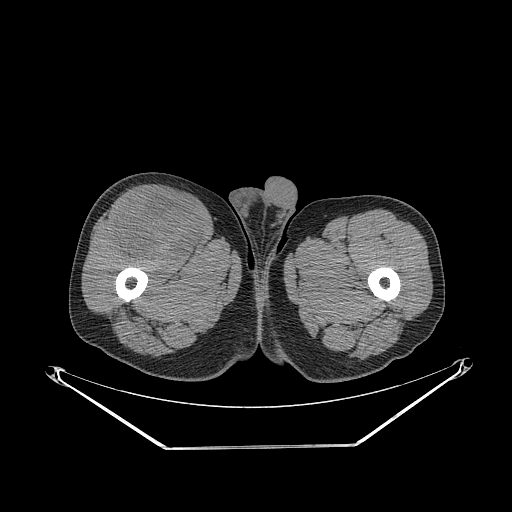
CT of an extremity soft-tissue mass (from a PET/CT study), one axial slice; slice 285 of 311 in the series (ordered by position); reconstruction kernel STANDARD; 140 kVp; soft-tissue window (W 400 / L 40 HU); 3.75 mm slice thickness; 512 × 512 image matrix, field of view 500 × 500 mm. Male patient. From the clinical record (not read from this slice): histological type: pleiomorphic leiomyosarcoma; grade: intermediate; site of the primary tumour: right thigh.
Outlined on this slice (expert contour drawn on MRI and transferred to this co-registered scan by the dataset authors):
- gross tumour volume including surrounding oedema: bounding box <112,192,204,261> (left, top, right, bottom; pixels)
- gross tumour volume (mass): <112,192,204,261>